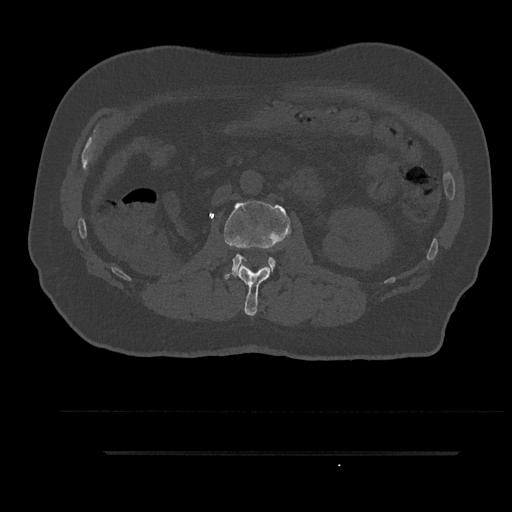
CT including the spine, one axial slice. Position 139 of 797 along the scan axis. Bone window (W 1800 / L 400 HU). 0.5 mm slice thickness. 512 × 512 image matrix, field of view 432 × 432 mm. Patient: male, 63 years. Case-level facts recorded for this patient, not image findings: primary cancer: renal; vertebrae with lytic lesions (as recorded): T8.
Structures marked on this image (semi-automatically segmented with operator editing):
- L1 vertebra: bounding box (x1, y1, x2, y2) in pixels: (236, 264, 273, 316)
- L2 vertebra: (224, 201, 291, 279)